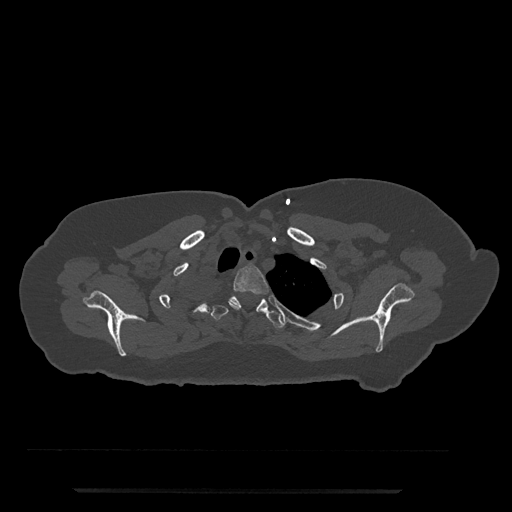
CT including the spine, one axial slice; position 655 of 797 along the scan axis; reconstruction kernel Br40s/3; bone window (W 1800 / L 400 HU); 0.5 mm slice thickness; 512 × 512 image matrix, field of view 440 × 440 mm. Female patient, age 51 years. From the clinical record (not read from this slice): primary cancer: neuro; vertebrae with lytic lesions (as recorded): T8.
Structures marked on this image (semi-automatic segmentation, software-assisted and operator-edited):
- T2 vertebra: box from (x=229, y=265) to (x=269, y=310) px
- T3 vertebra: (x=210, y=296)–(x=284, y=329)